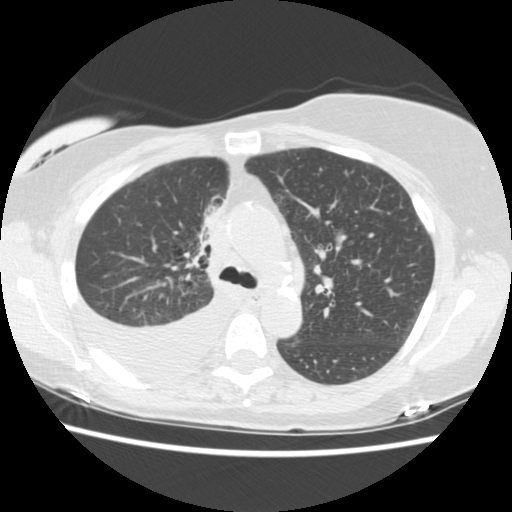
Chest CT (low-dose screening protocol), one axial image; third annual screen; lung window (W 1500 / L -600 HU); standard (soft-tissue) reconstruction kernel (STANDARD); 120 kVp; slice 56 of 157 in the series. Female participant, aged 56 years at enrolment. Current smoker at enrolment.
- Expert reader's lesion annotation, bounding box <181,190,239,255> (left, top, right, bottom; pixels).
- The screening reader recorded 2 non-calcified nodules or masses ≥4 mm on this exam (right middle lobe, right lower lobe); which of them this box marks is not recorded.
- Official screen result: positive, other.
- Lung cancer was diagnosed 160 days after this screen: adenocarcinoma, NOS, right upper lobe, stage IIIB (AJCC 6th edition), 8 mm at pathology.